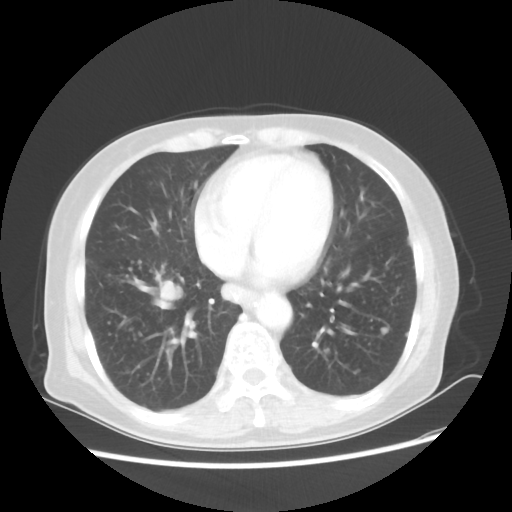
Chest CT, one axial slice; slice 20 of 56 in the series (ordered by position); reconstruction kernel STANDARD; 80 kVp; lung window (W 1500 / L -600 HU); 5 mm slice thickness; 512 × 512 image matrix. Female patient, age 68 years. From the clinical record (not read from this slice): clinical TNM (as recorded): T1c N3 M0.
Outlined on this slice (bounding box drawn by a radiologist):
- lung tumour (recorded histology: squamous cell carcinoma): bounding box <145,274,191,316> (left, top, right, bottom; pixels)